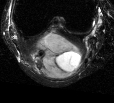
MRI of an extremity soft-tissue mass, one axial slice; T2-weighted fat-saturated; MR volume resampled by the dataset authors to the PET/CT grid (not the native acquisition matrix); 114 × 103 image matrix, field of view 111 × 101 mm. Female patient. Case-level facts recorded for this patient, not image findings: histological type: liposarcoma; site of the primary tumour: right thigh.
Structures marked on this image (expert contour drawn on MRI and transferred to this co-registered scan by the dataset authors):
- gross tumour volume (mass): box from (x=29, y=32) to (x=83, y=78) px